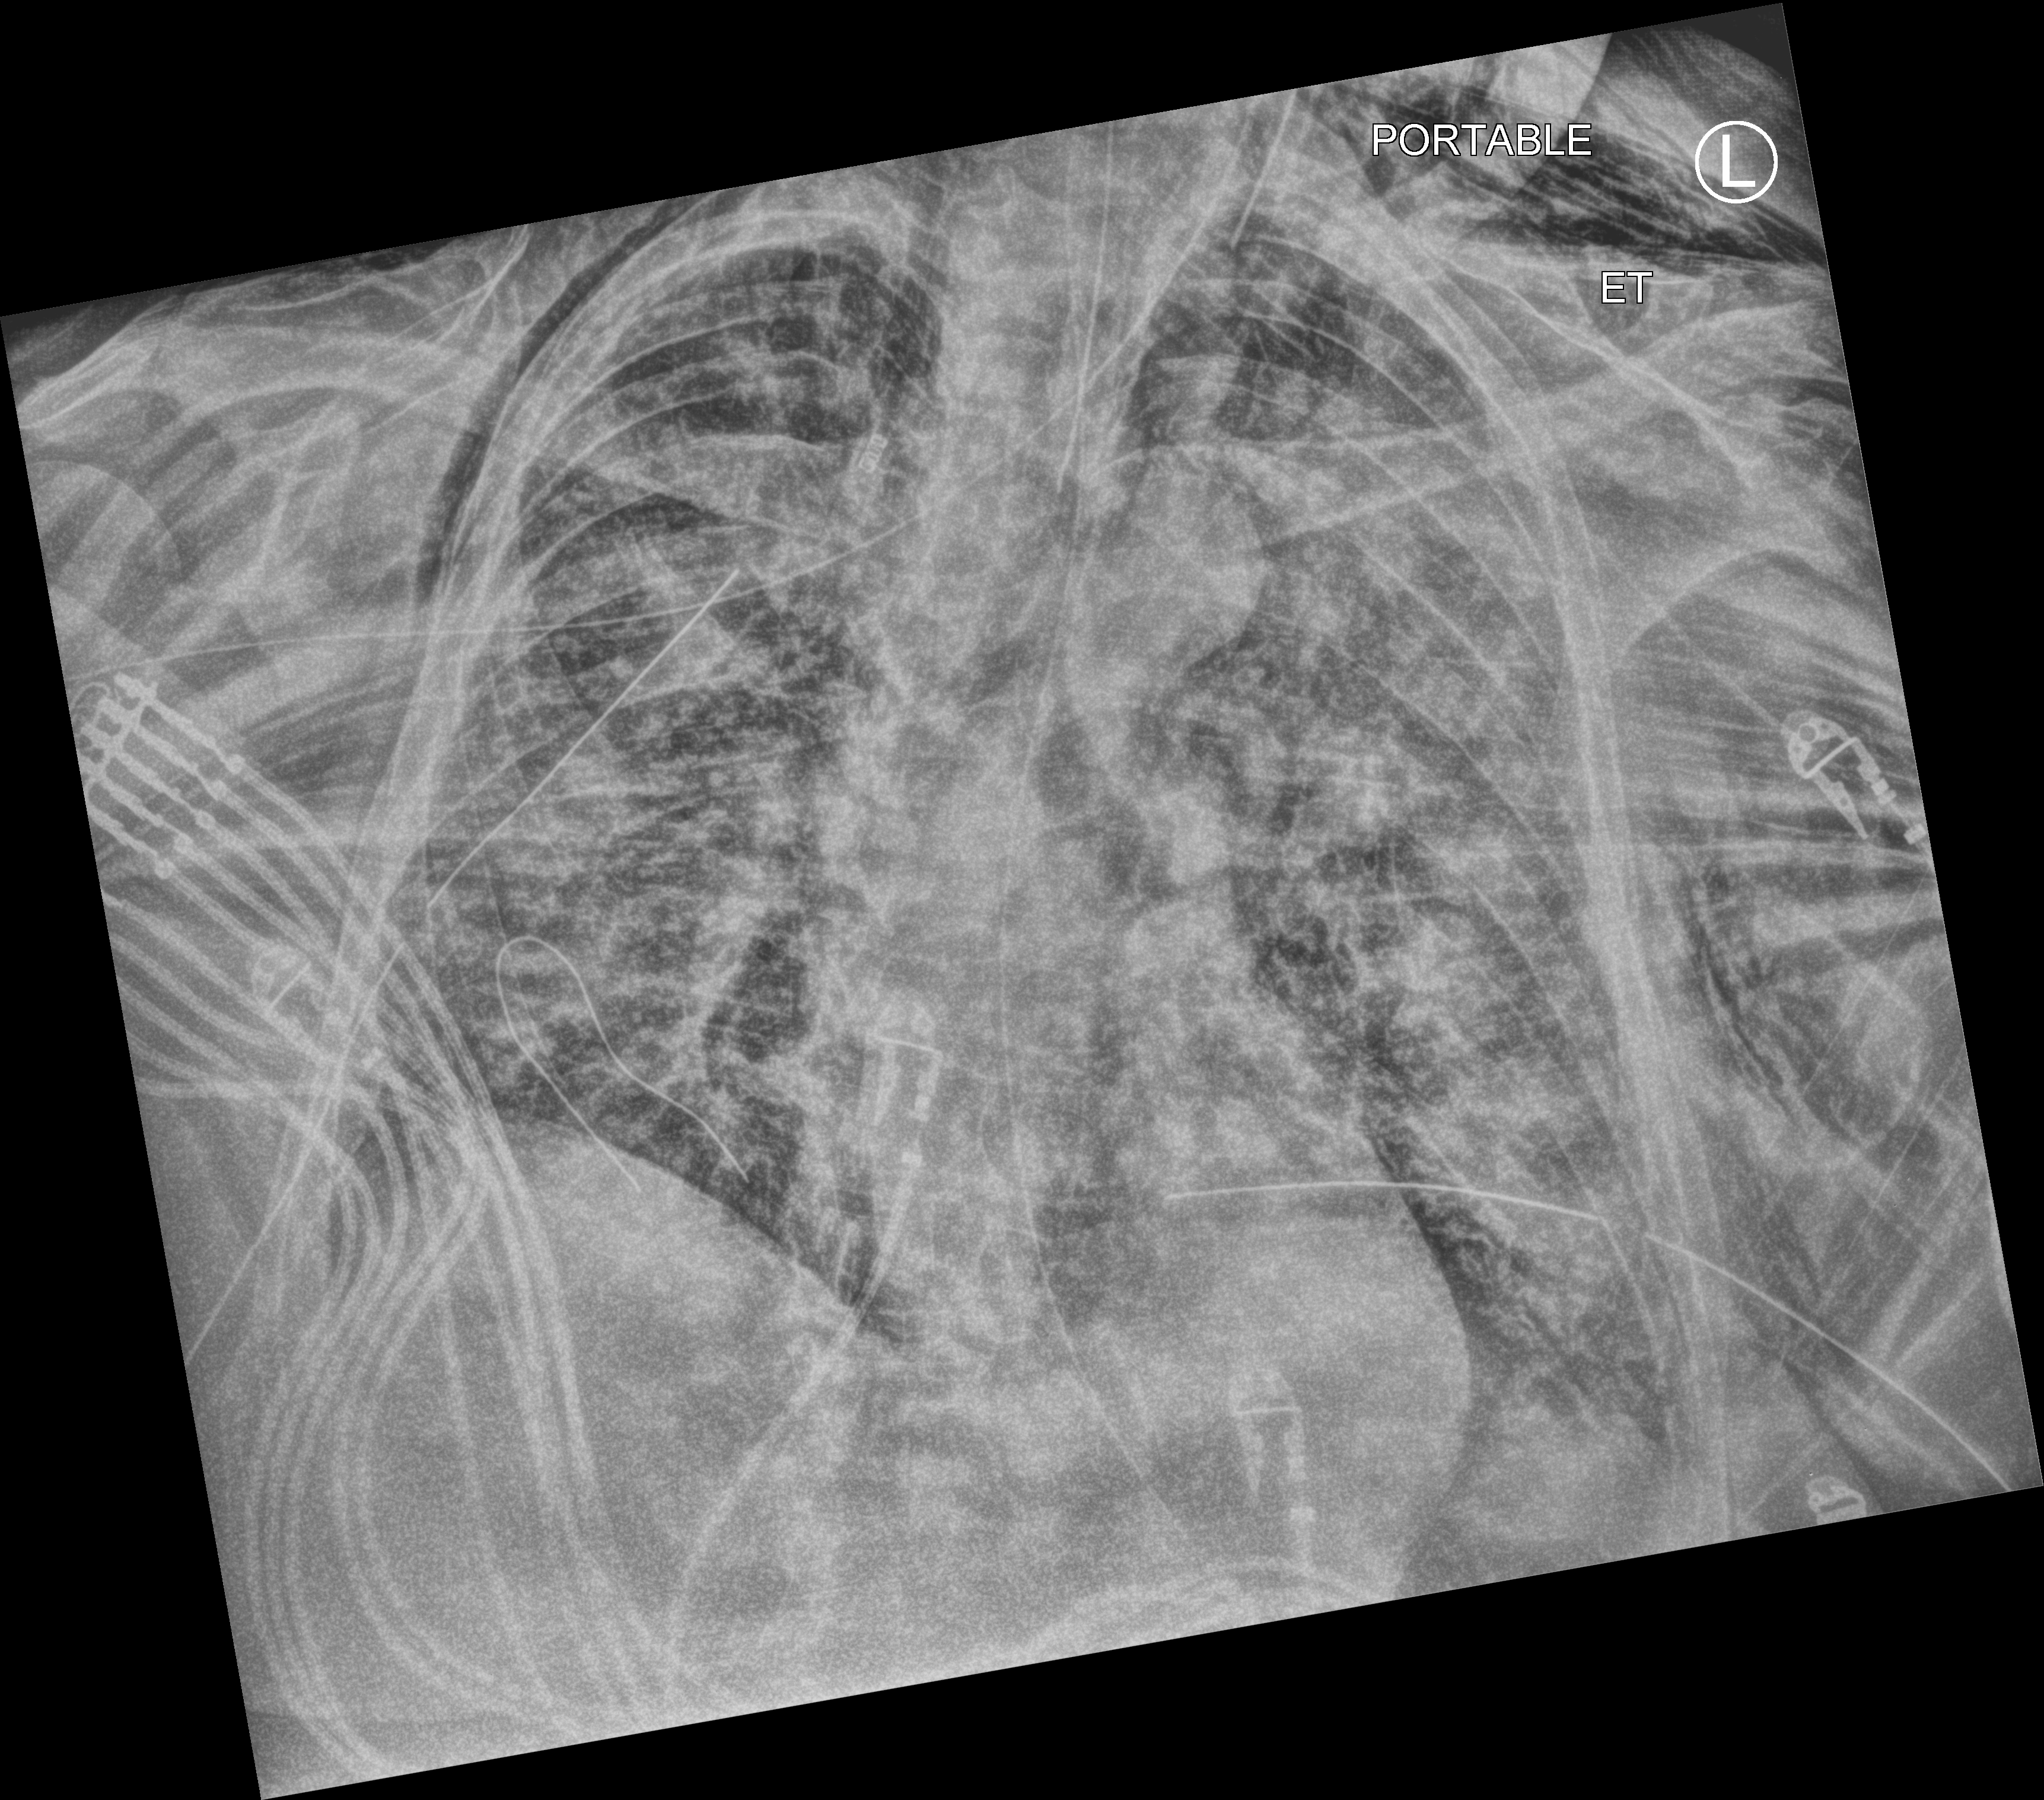
Portable chest radiograph; anteroposterior (AP) projection. Adult patient hospitalised with COVID-19, age 18–59 years.
Admission-level facts for this patient (not findings on this image; timing relative to this image not recorded): length of hospital stay: 28 days; hypertension (admission record): yes.